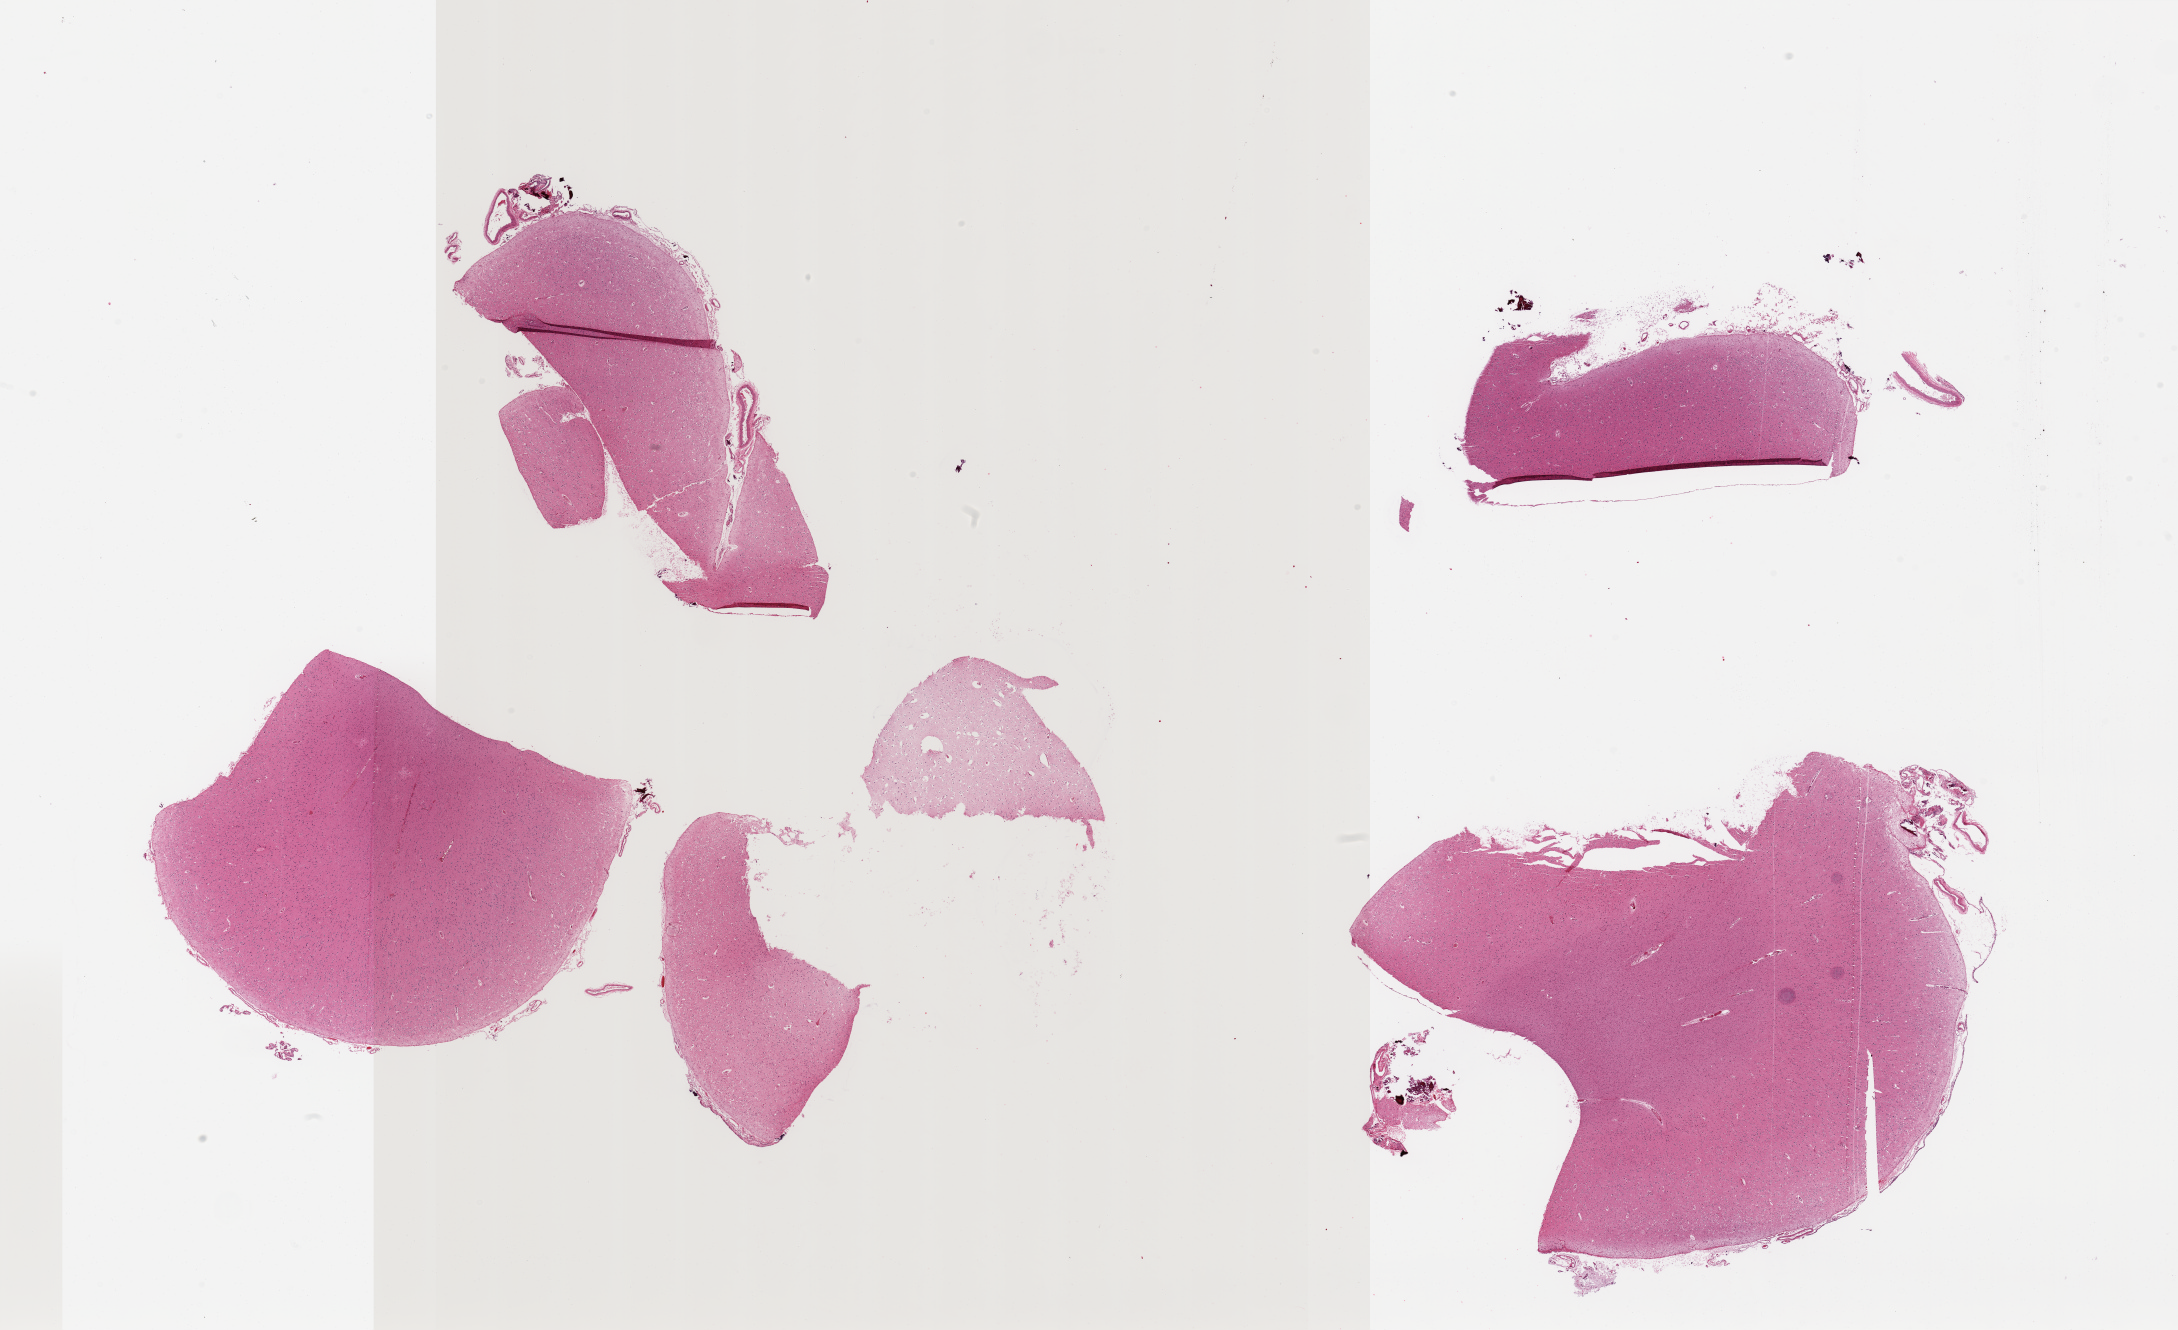
Digitized haematoxylin and eosin-stained section, low-resolution overview of the scanned area, about 34.5 x 21.0 mm; PAXgene-fixed, paraffin-embedded tissue; sampled site (target tissue): cerebral cortex; donor tissue sample. Donor: female.
- pathologist's review note for this sample: 4 pieces (fragmented), no abnormalities